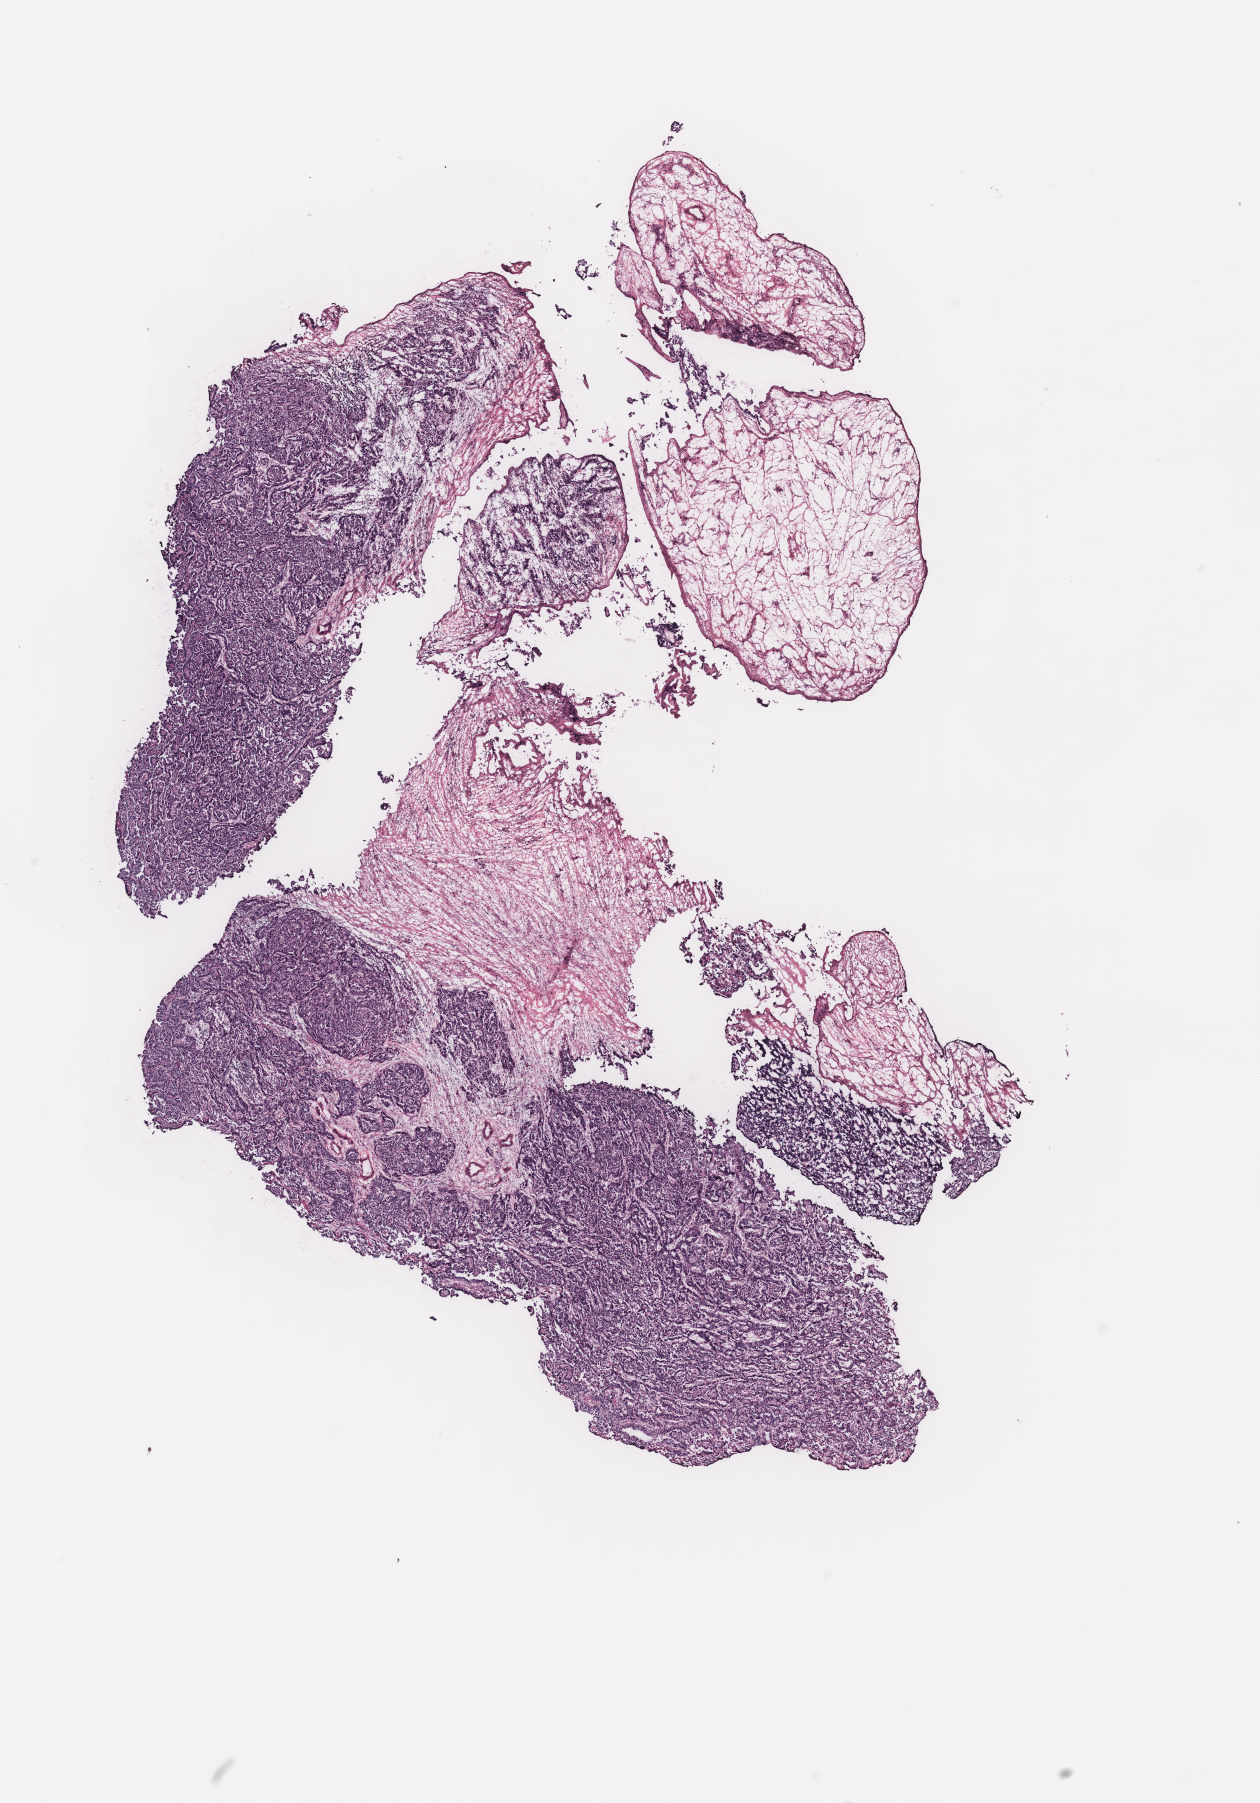
Hematoxylin and eosin (H&E) stained whole-slide image — shown as a low-resolution overview of the whole scanned area (about 10.1 x 14.4 mm, from a 40x scan). Ovary, tissue type not recorded. Female patient.
Patient diagnosis: Serous adenocarcinoma, NOS.